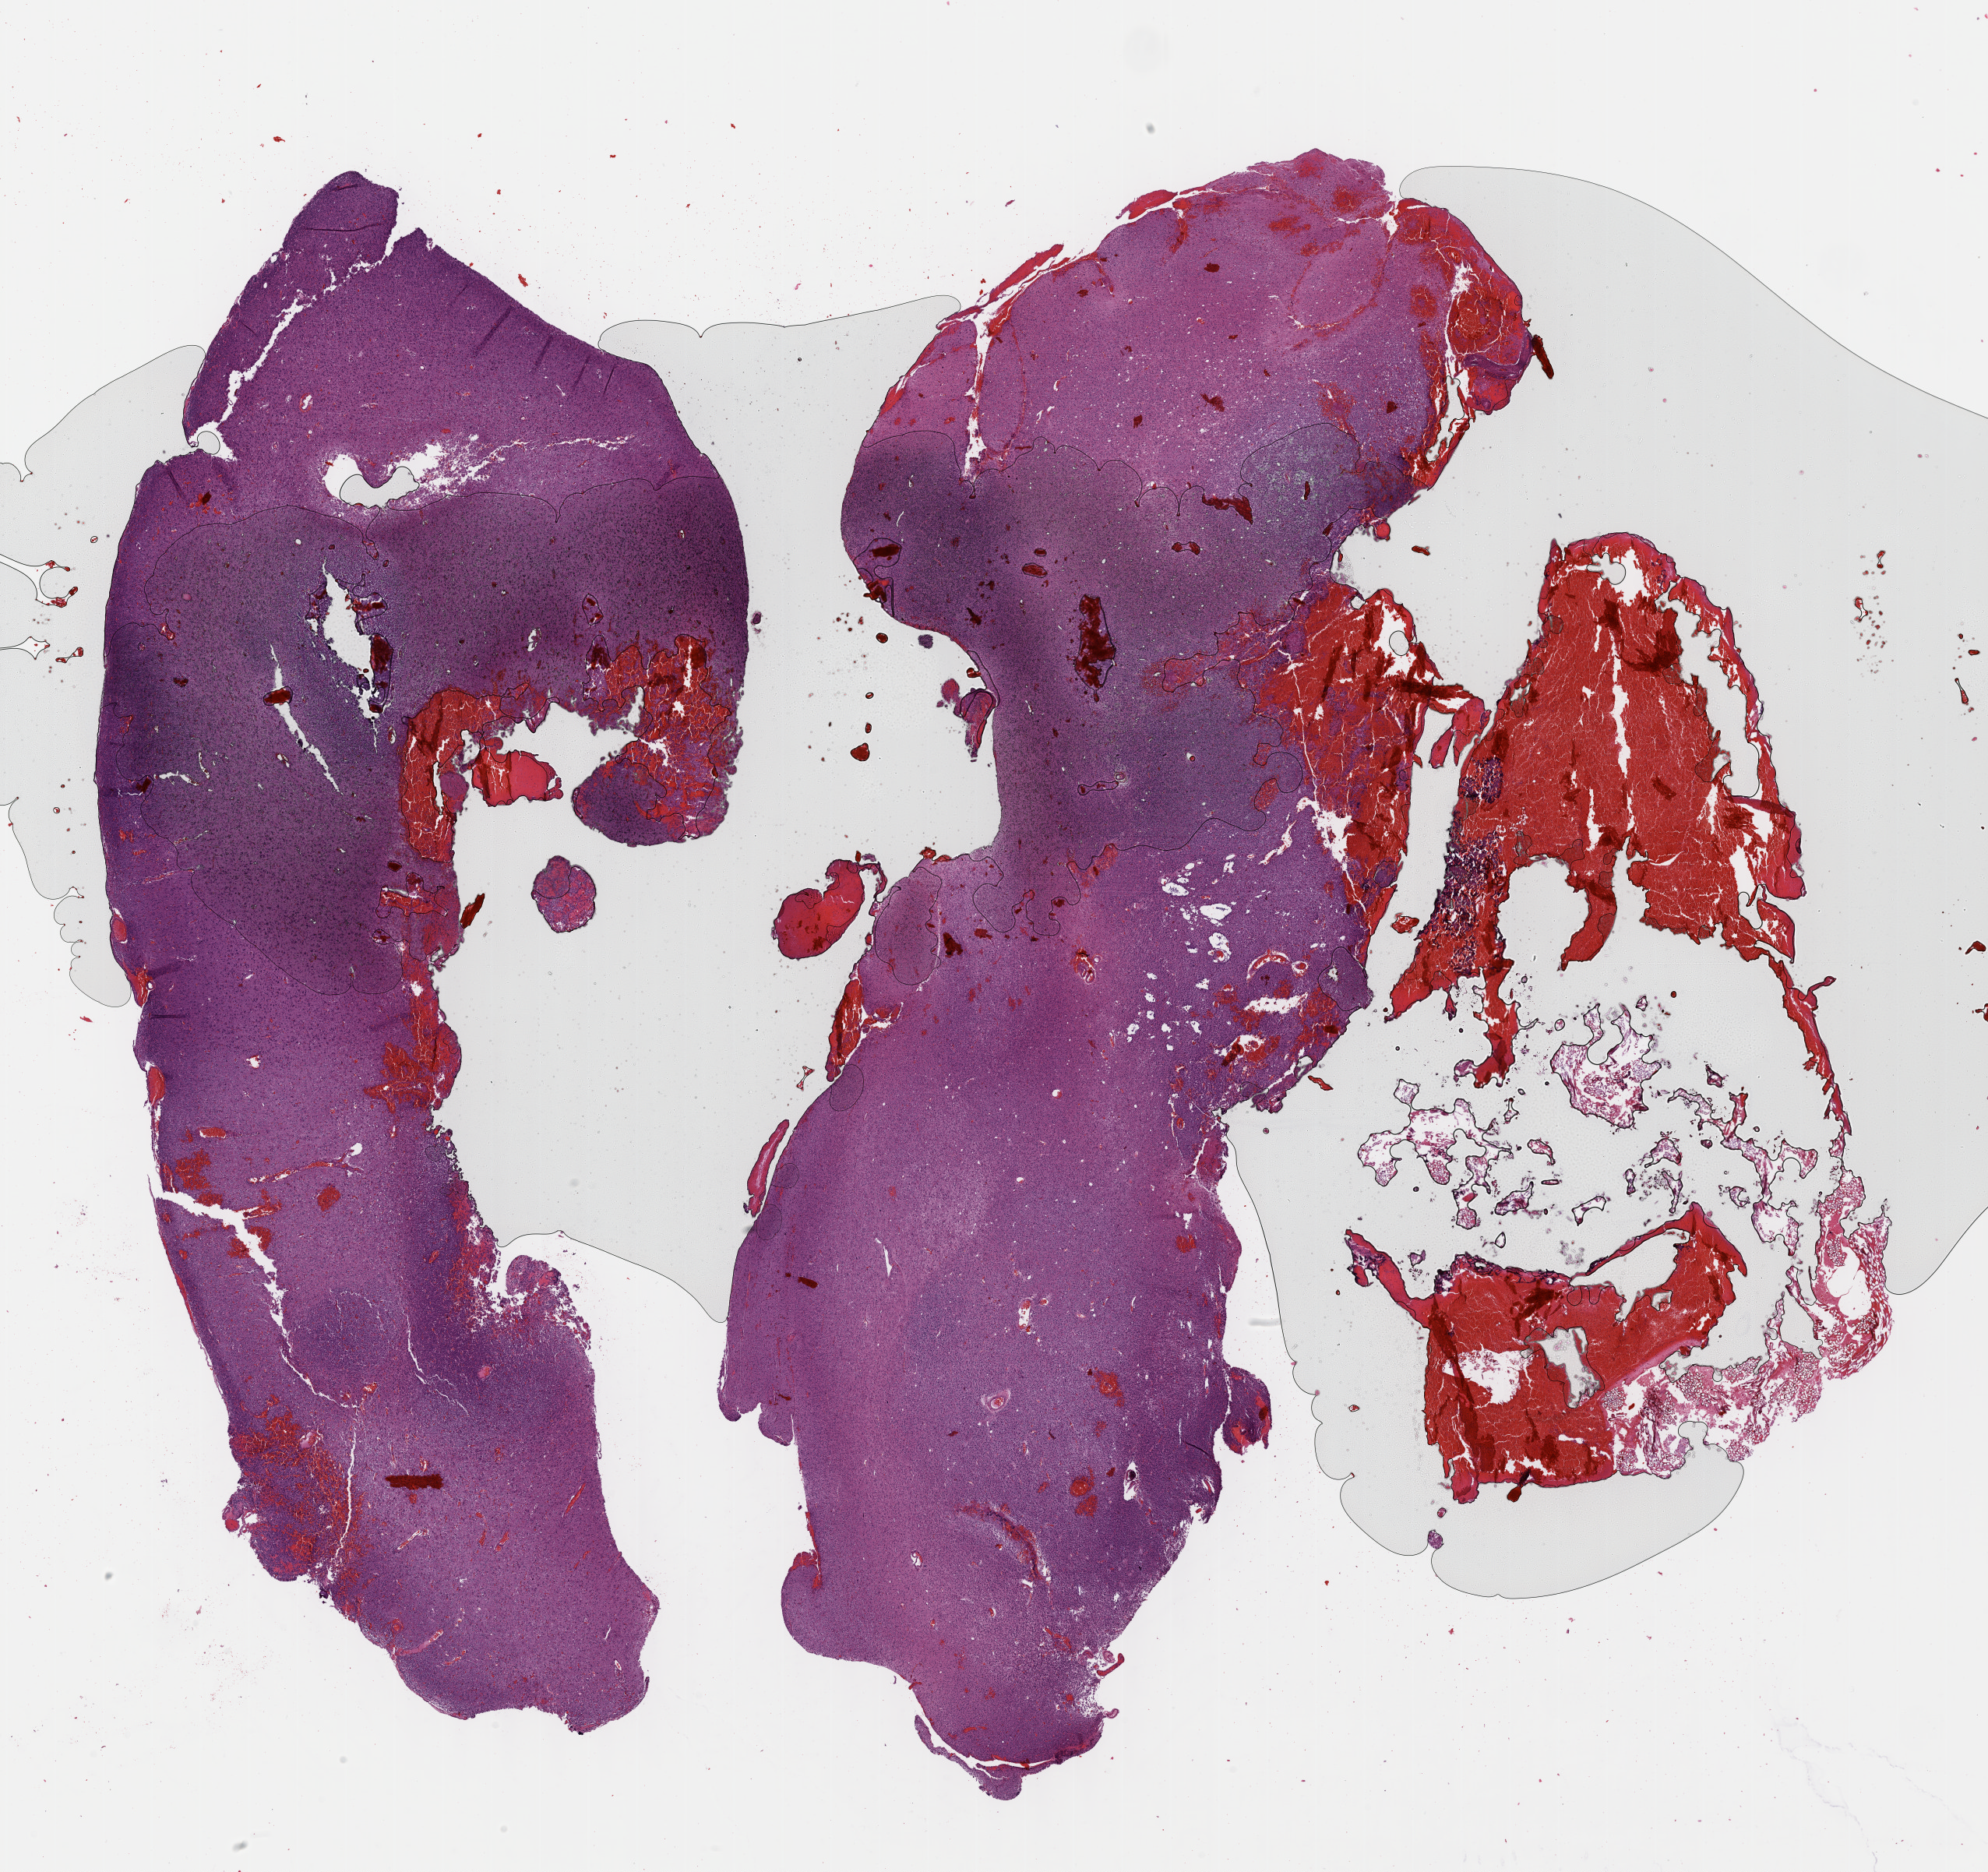
Whole-slide histology image, H&E-stained — low-resolution overview of the scanned area, about 20.6 x 19.4 mm (slide scanned at 40x), FFPE section, brain, primary tumour sample. Male, age 60 years at initial diagnosis. Histologic grade: G3 (poorly differentiated).
- diagnosis: Oligodendroglioma, anaplastic (cerebrum)
- laterality: right